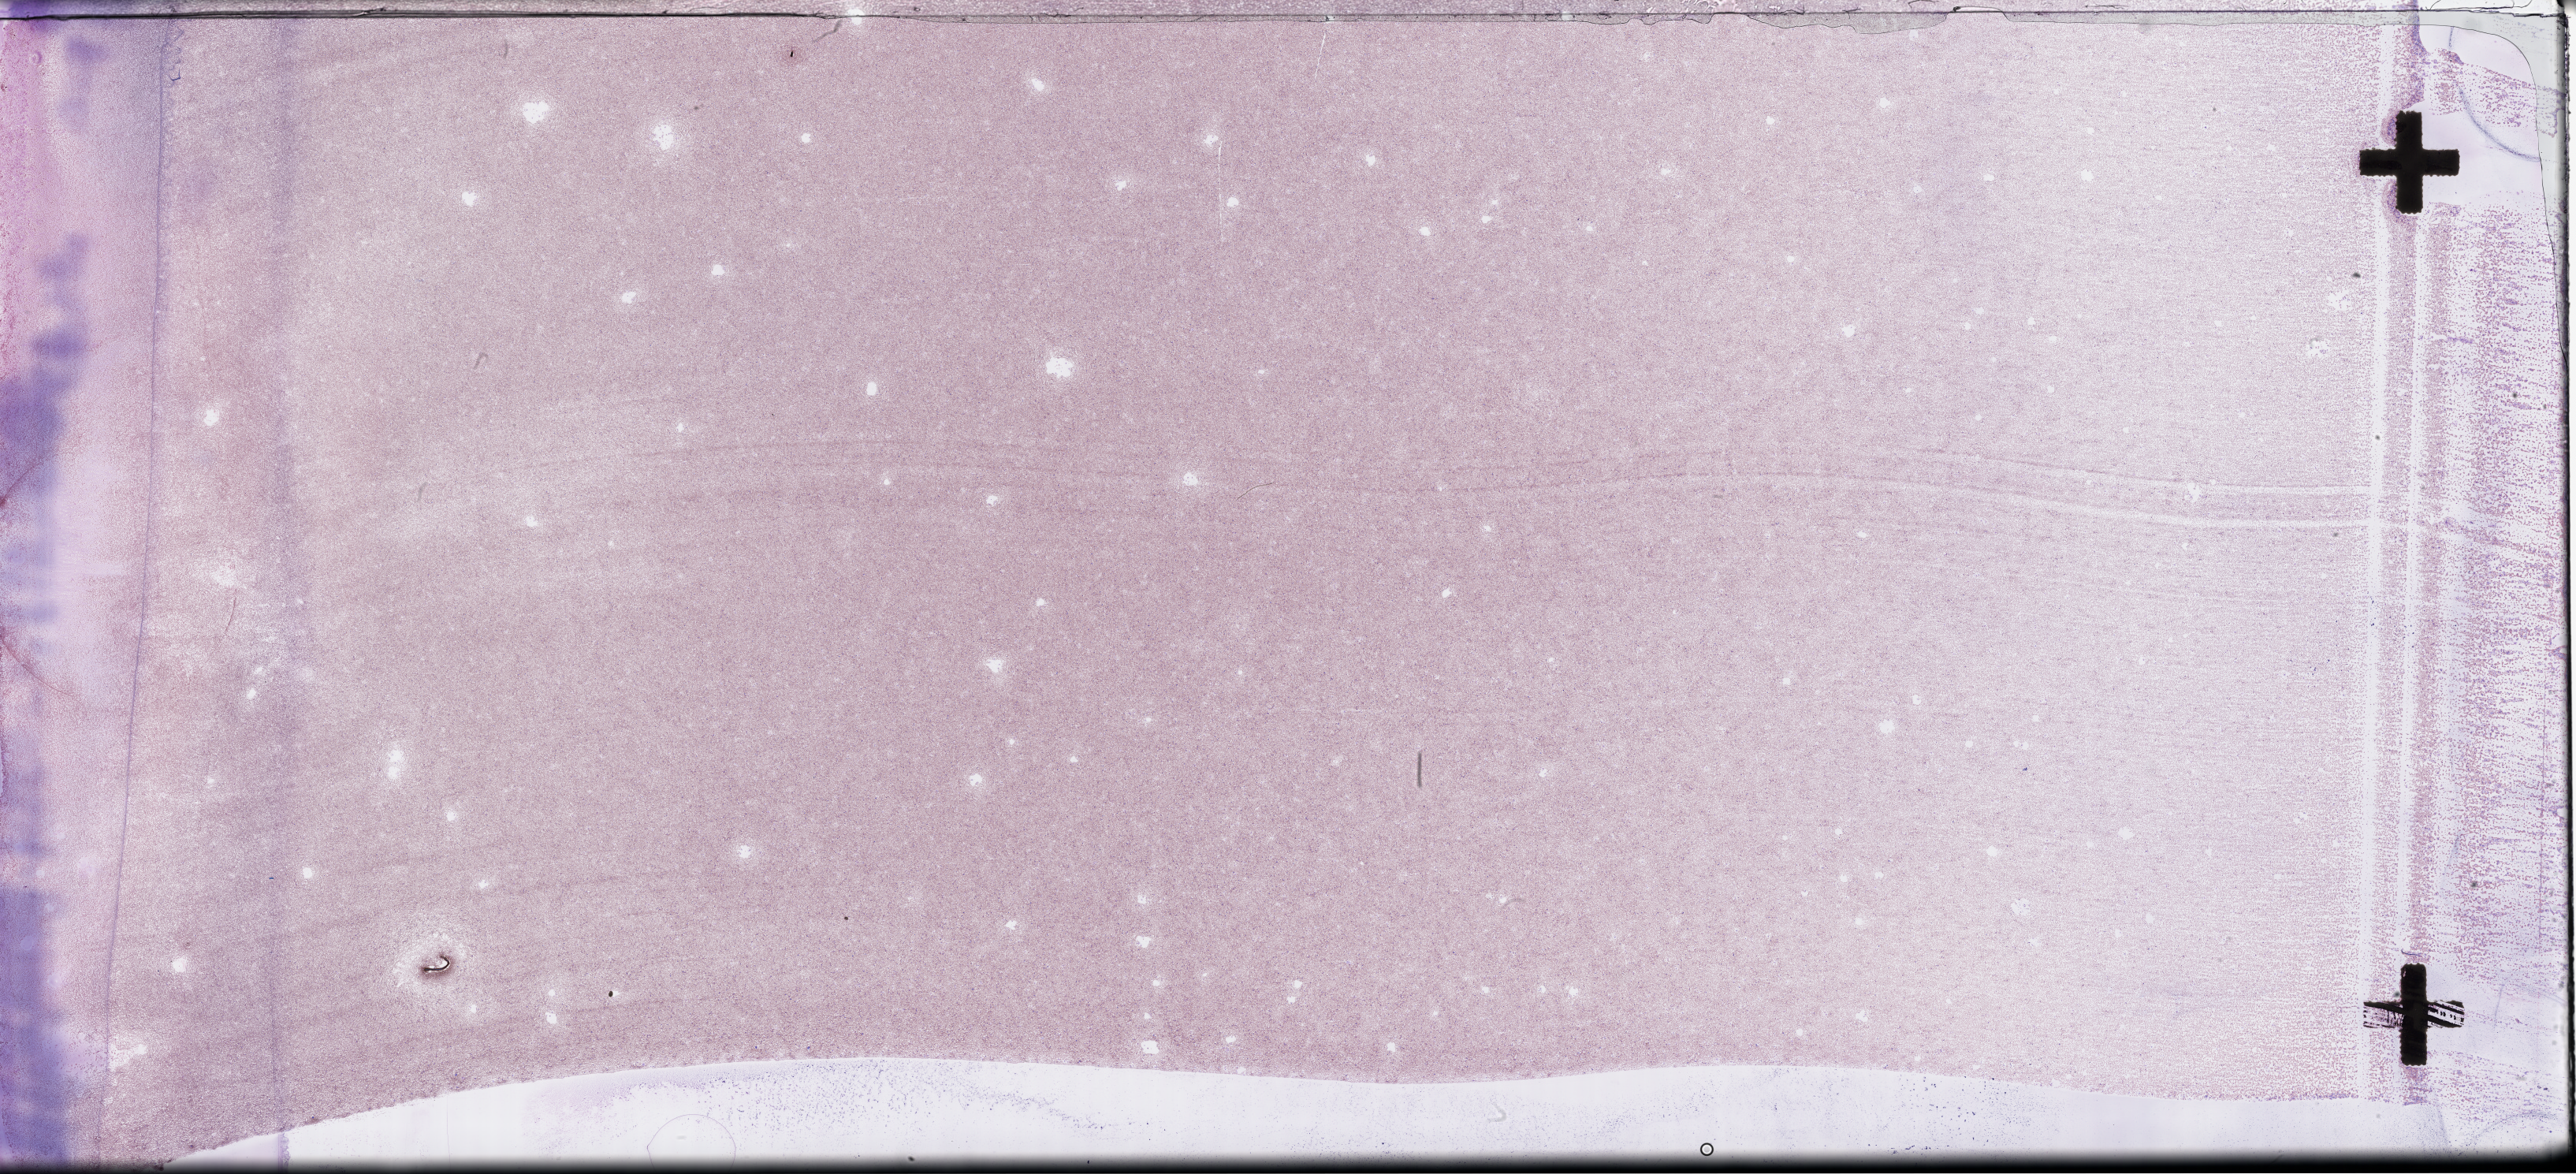
Whole-slide image of a bone marrow smear, Wright–Giemsa stain, whole scanned area (about 52.8 x 24.0 mm) shown as a low-resolution overview, collected on treatment. Male patient.
From a patient with: Plasma Cell Myeloma.